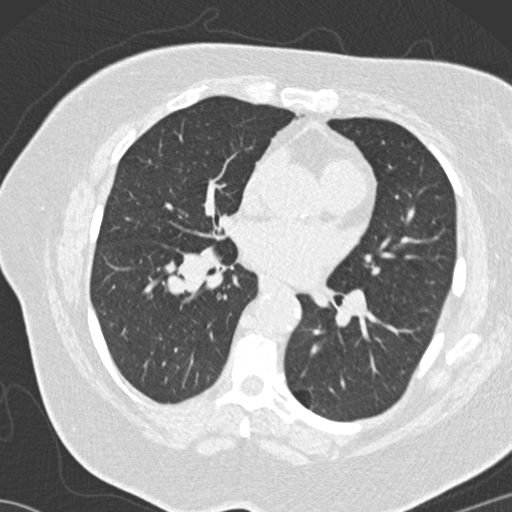
Low-dose screening chest CT, one axial slice; slice 69 of 146 in the series (ordered by position); reconstruction kernel B30f; 120 kVp; lung window (W 1500 / L -600 HU); 512 × 512 image matrix.
Annotated regions visible in this slice (expert manual segmentation):
- lesion 4 (tumor, lower lobe of right lung): bounding box <164,261,185,296> (left, top, right, bottom; pixels)